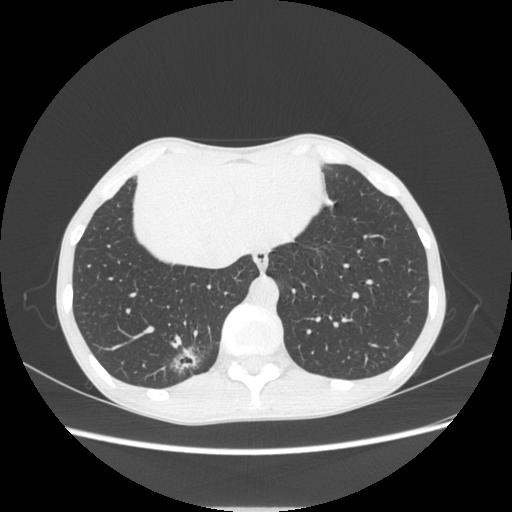
Chest CT, one axial slice; position 65 of 272 along the scan axis; reconstruction kernel STANDARD; lung window (W 1500 / L -600 HU); 512 × 512 image matrix. Patient: female, 51 years. Case-level facts recorded for this patient, not image findings: clinical TNM (as recorded): T1c N0 M0; histopathological grade: G2-3.
Annotated regions visible in this slice (bounding box drawn by a radiologist):
- lung tumour (recorded histology: adenocarcinoma): bounding box <169,340,210,383> (left, top, right, bottom; pixels)